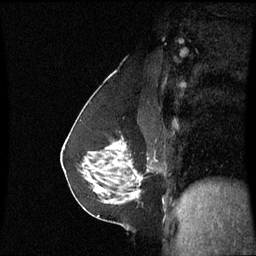
Breast MRI (dynamic contrast-enhanced), one sagittal slice. Position 35 of 60 along the scan axis. Dynamic contrast-enhanced series, image 2 of 3 at this slice position (ordered by acquisition). 1.5 T. TE 4.2 ms, TR 8.9 ms. 2.2 mm slice thickness. 256 × 256 image matrix, field of view 220 × 220 mm. Female patient, age 58 years. Case-level facts recorded for this patient, not image findings: setting: breast cancer imaged before/during neoadjuvant chemotherapy; receptor status: triple-negative.
Outlined on this slice (semi-automatically segmented with operator editing):
- analysis volume of interest (the breast-tissue region the enhancement analysis was run in; not a lesion): box from (x=90, y=142) to (x=149, y=193) px
- tumour enhancement mask (voxels above the 70 % enhancement threshold inside the analysis volume of interest): (x=130, y=166)–(x=139, y=193)